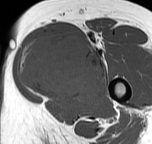
MRI of an extremity soft-tissue mass, one axial slice; slice 34 of 57 in the series (ordered by position); MR volume resampled by the dataset authors to the PET/CT grid (not the native acquisition matrix); 152 × 144 image matrix. Female patient. From the clinical record (not read from this slice): histological type: pleiomorphic leiomyosarcoma; grade: intermediate; site of the primary tumour: left thigh.
Outlined on this slice (expert contour drawn on MRI and transferred to this co-registered scan by the dataset authors):
- gross tumour volume including surrounding oedema: bounding box [x1, y1, x2, y2] px = [18, 35, 105, 104]
- gross tumour volume (mass): [18, 37, 105, 104]